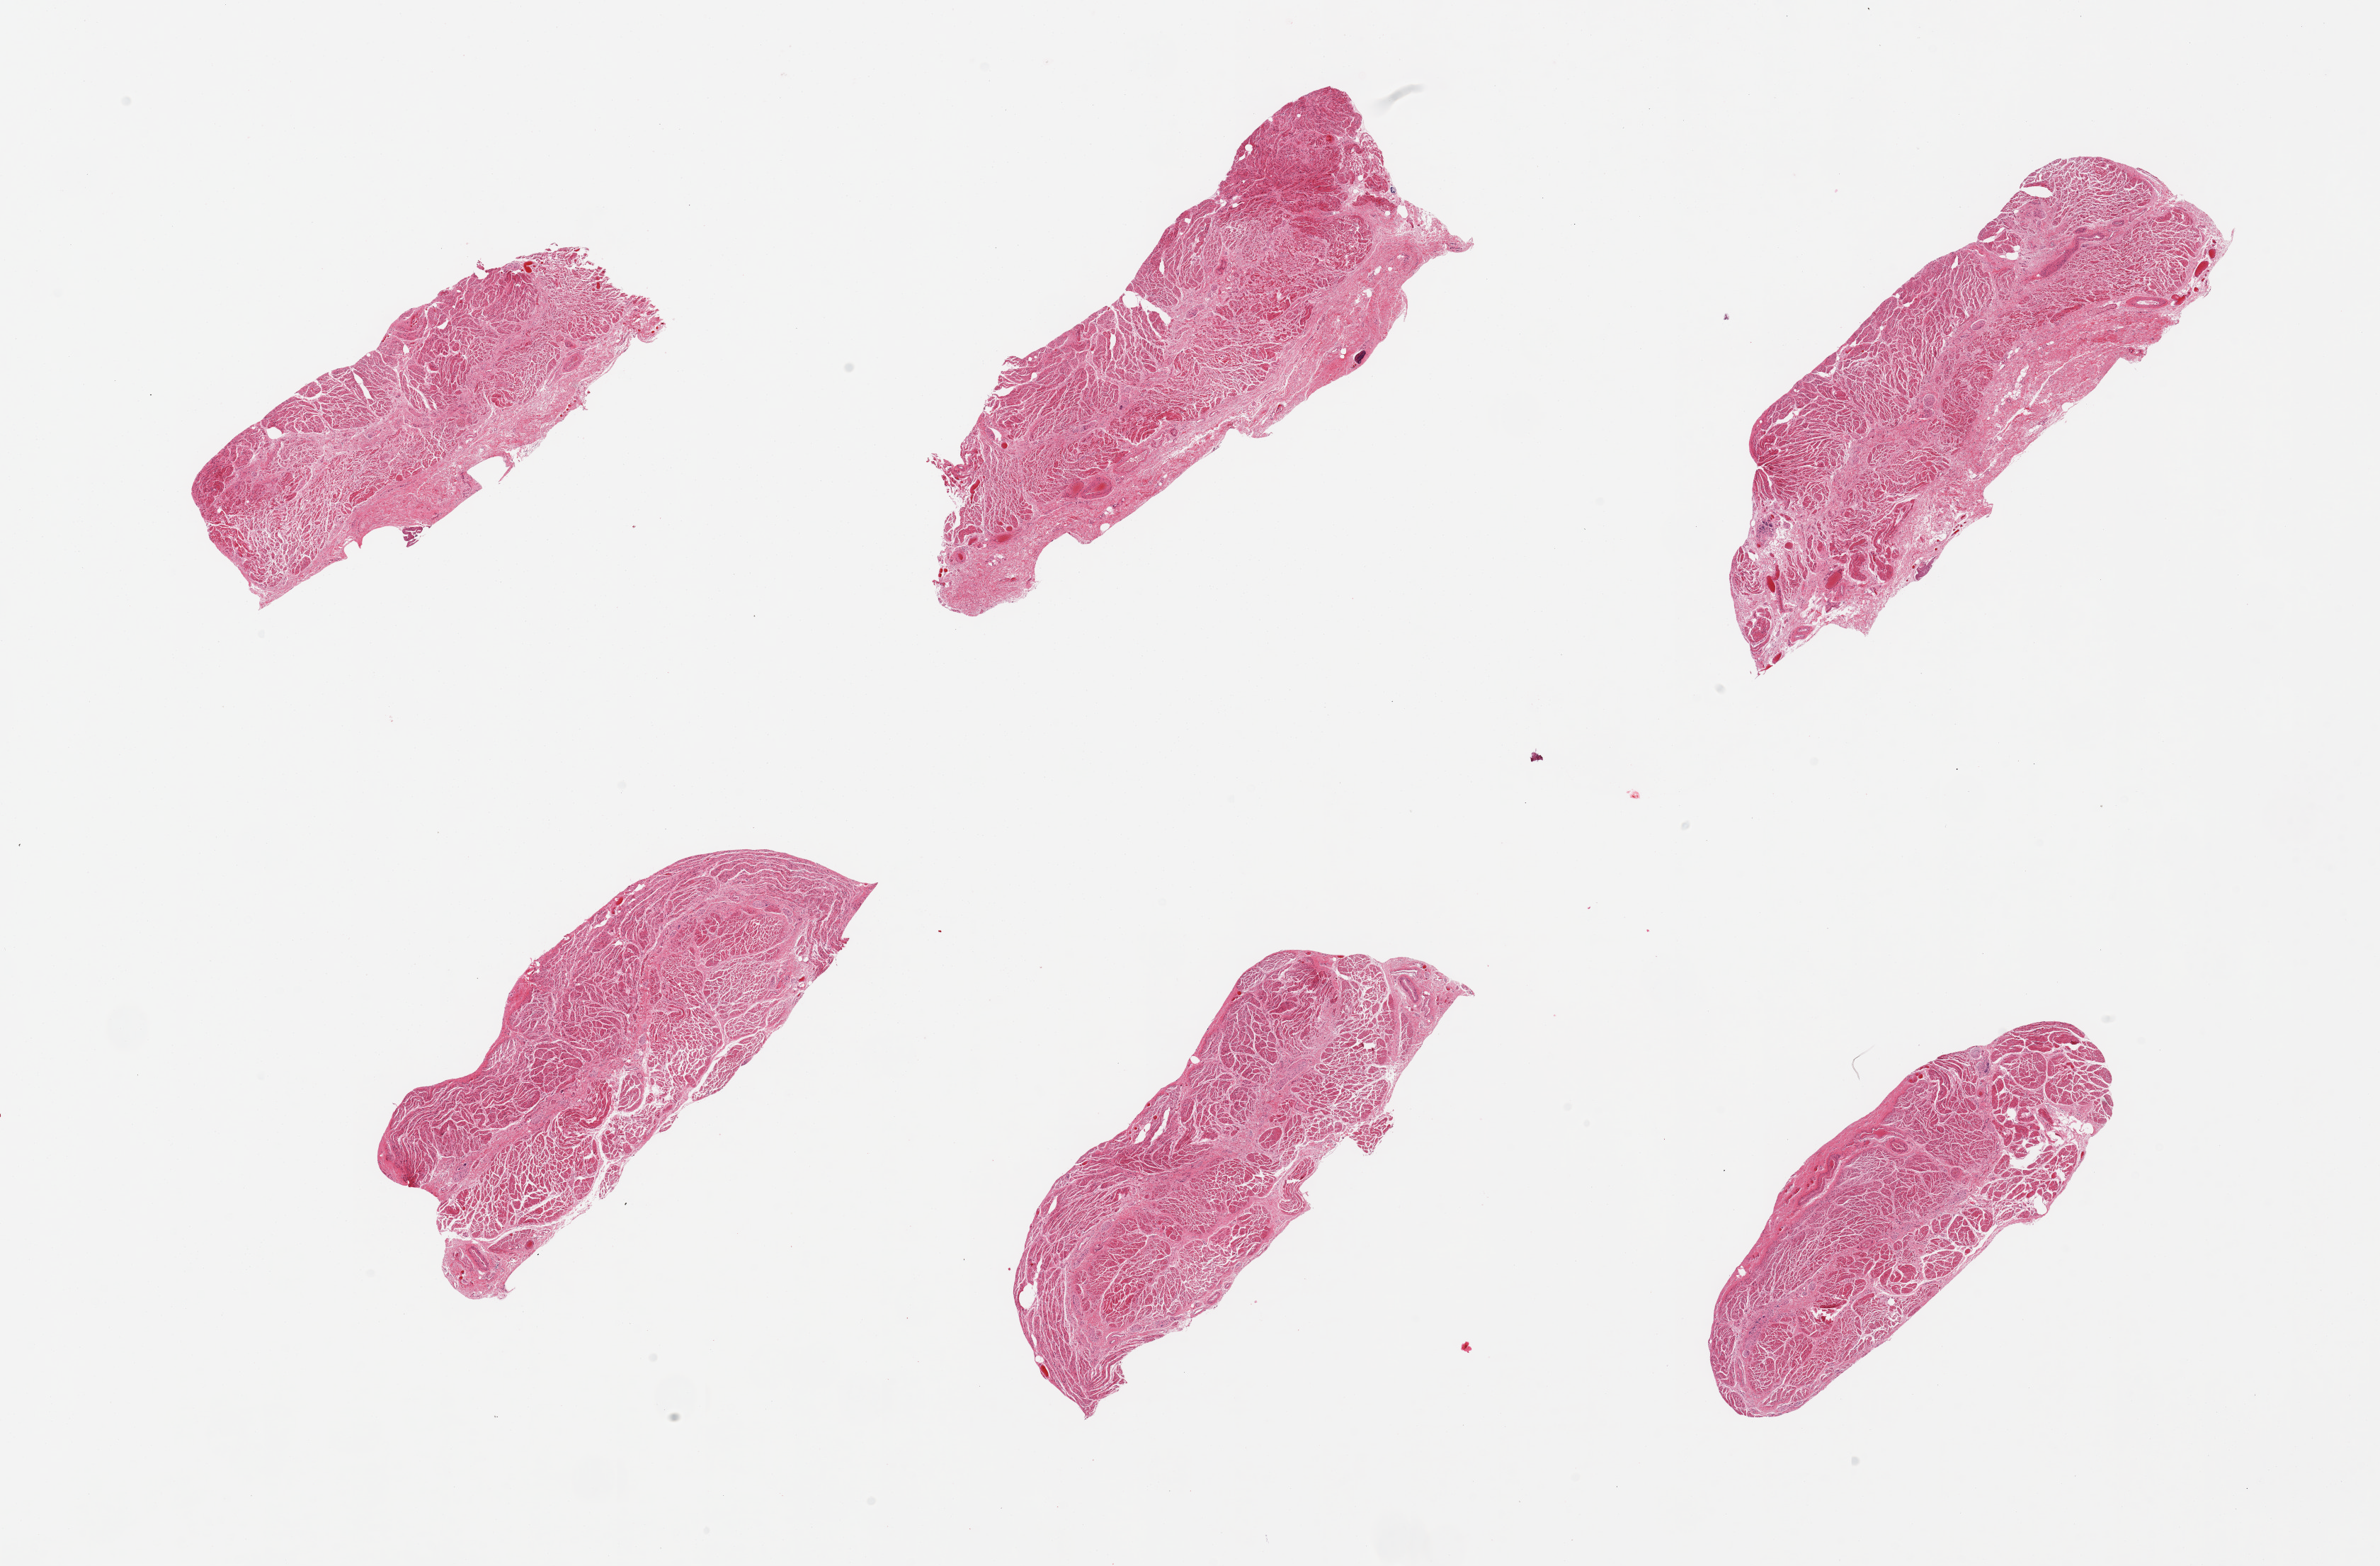
Digitized hematoxylin and eosin (H&E)-stained section, brightfield, a low-resolution overview of the entire scanned area, about 26.6 x 17.5 mm. PAXgene-fixed paraffin-embedded (PFPE) section. Target tissue: gastroesophageal junction. Donor tissue sample. Female donor.
Review note (as recorded): 6 pieces; well trimmed.